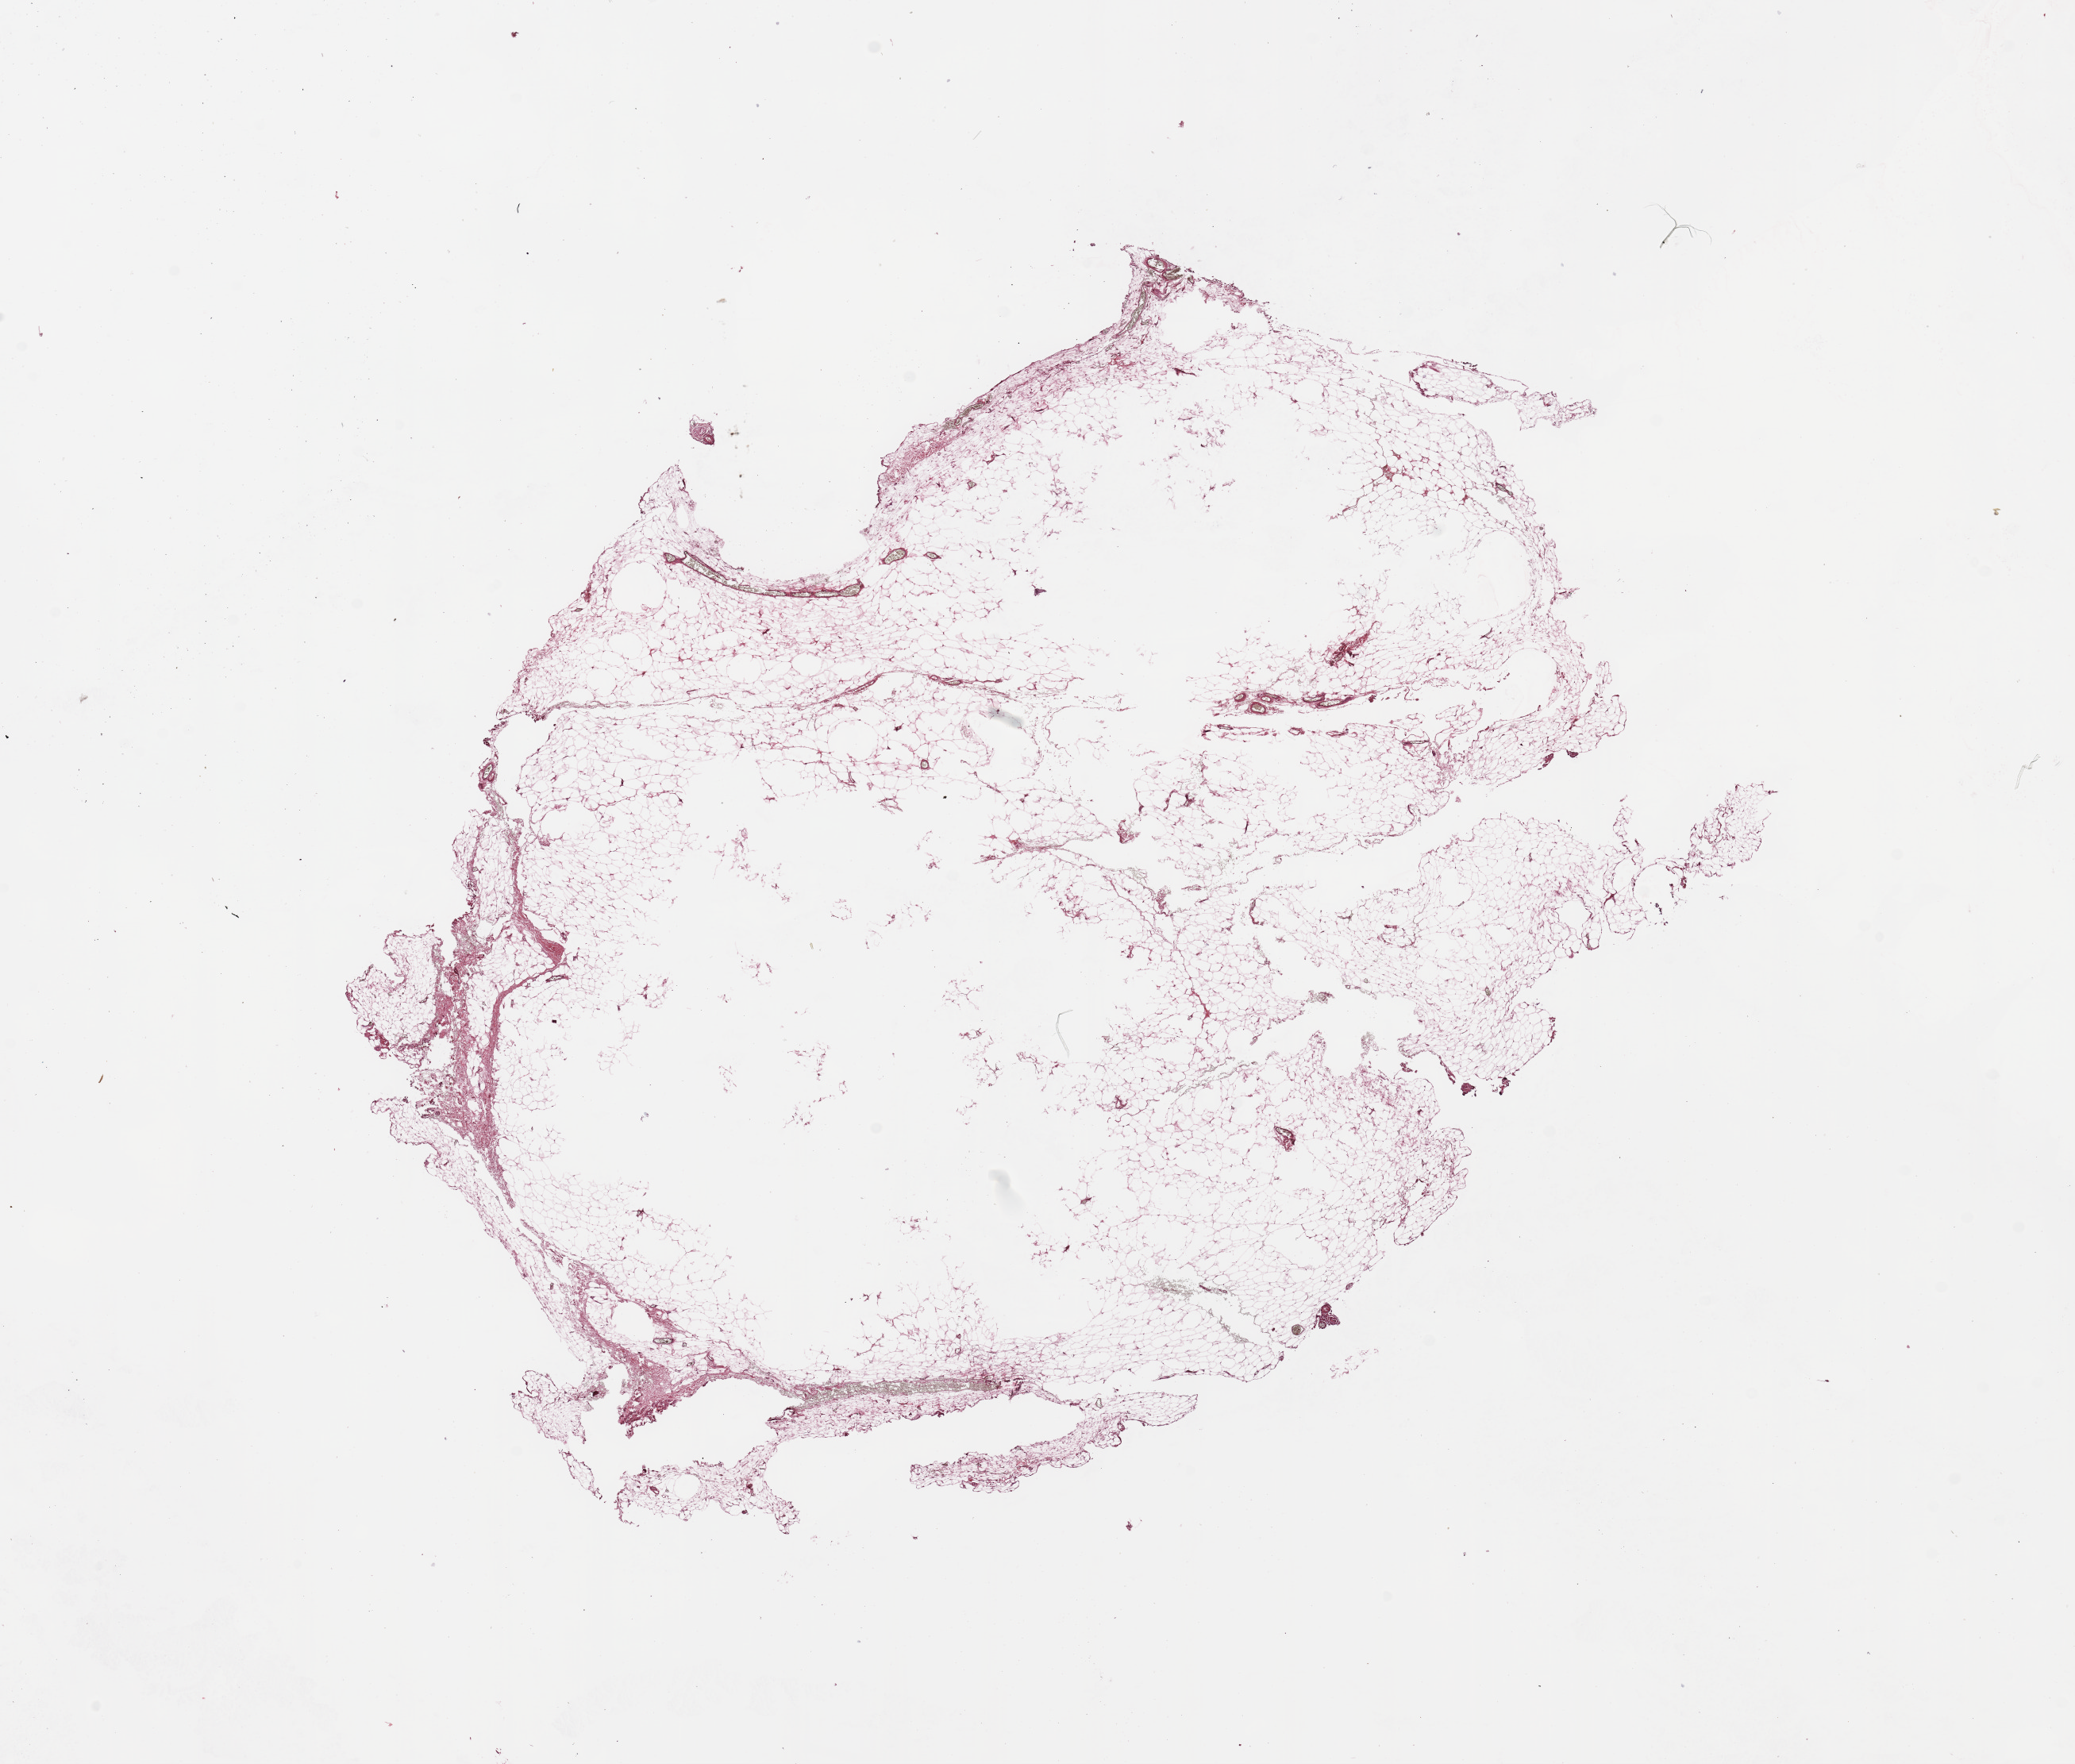
H&E-stained whole-slide image — whole scanned area (about 20.7 x 17.6 mm) shown as a low-resolution overview, normal (non-tumour) tissue (melanoma cohort); sampled site not recorded. 60-year-old male patient.
This section: normal (non-tumour) tissue from the same patient. Patient diagnosis (cohort enrolment): cutaneous melanoma (skin).